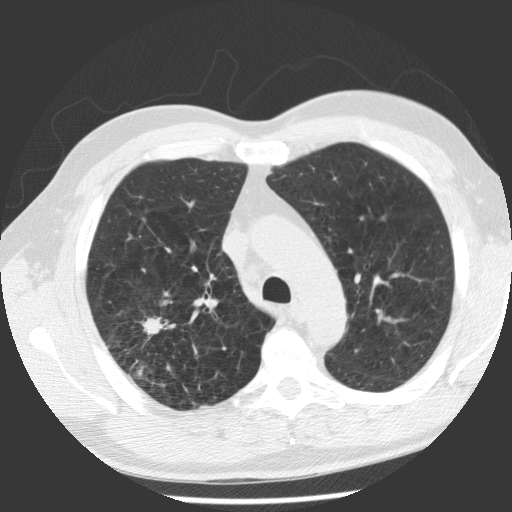
Low-dose screening chest CT, axial slice, first (baseline) screen, lung window (W 1500 / L -600 HU), slice 82 of 112 in the series, 512 × 512 image matrix, field of view 344 × 344 mm. Male, age 62 years at enrolment. Former smoker at enrolment.
Expert-annotated lung lesion, box from (x=113, y=301) to (x=190, y=377) px. The screening reader recorded 2 non-calcified nodules or masses ≥4 mm on this exam (right upper lobe, right upper lobe); which of them this box marks is not recorded. Official screen result: positive, change unspecified: nodule(s) >= 4 mm or enlarging nodule(s), mass(es), or other non-specific abnormalities suspicious for lung cancer.